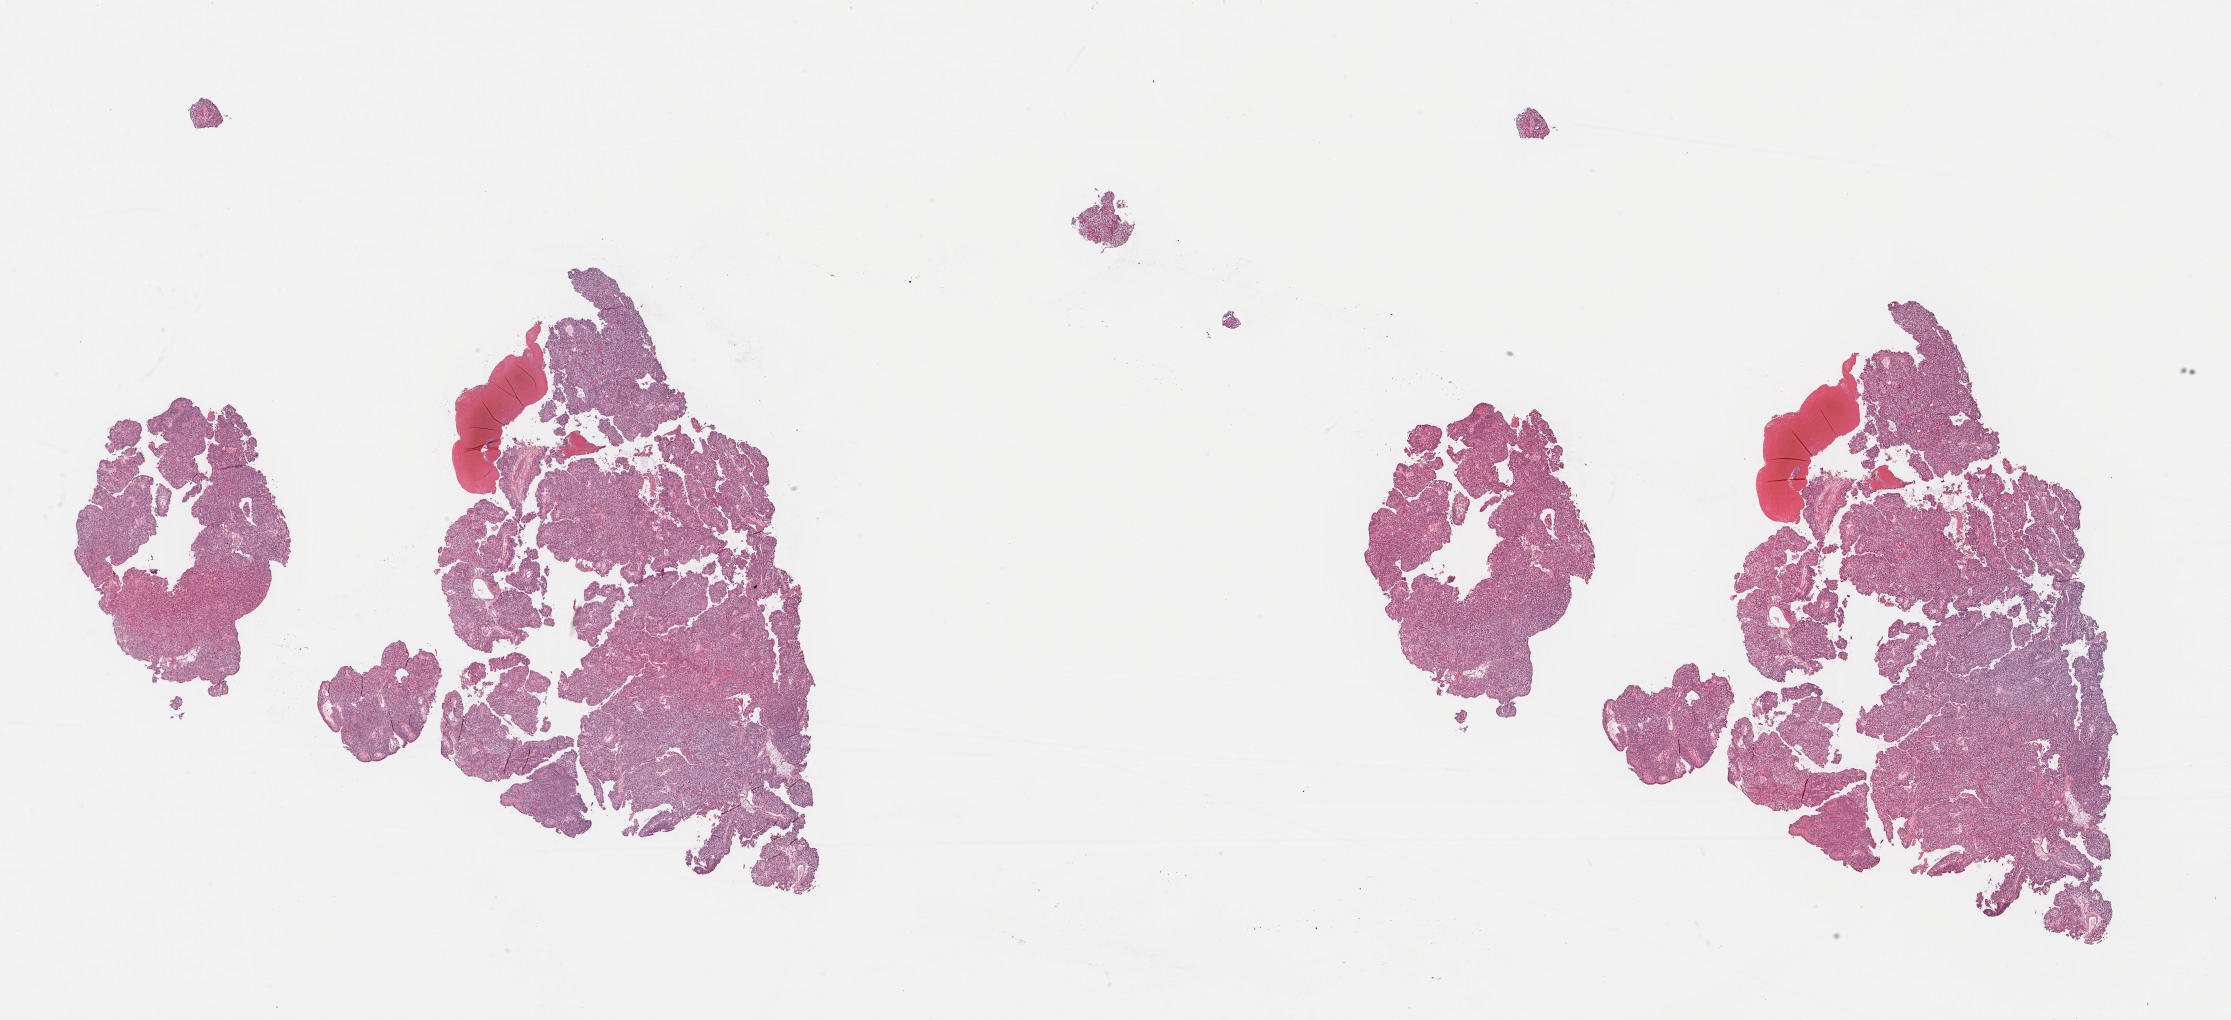
Whole-slide histology image, H&E, a low-resolution overview of the entire scanned area, about 35.2 x 16.1 mm (slide scanned at 40x). Formalin-fixed paraffin-embedded (FFPE) diagnostic section. Primary tumour sample from the bladder. Male, age 73 years at initial diagnosis.
Histologic diagnosis: Transitional cell carcinoma (dome of bladder). AJCC pathologic stage: I.